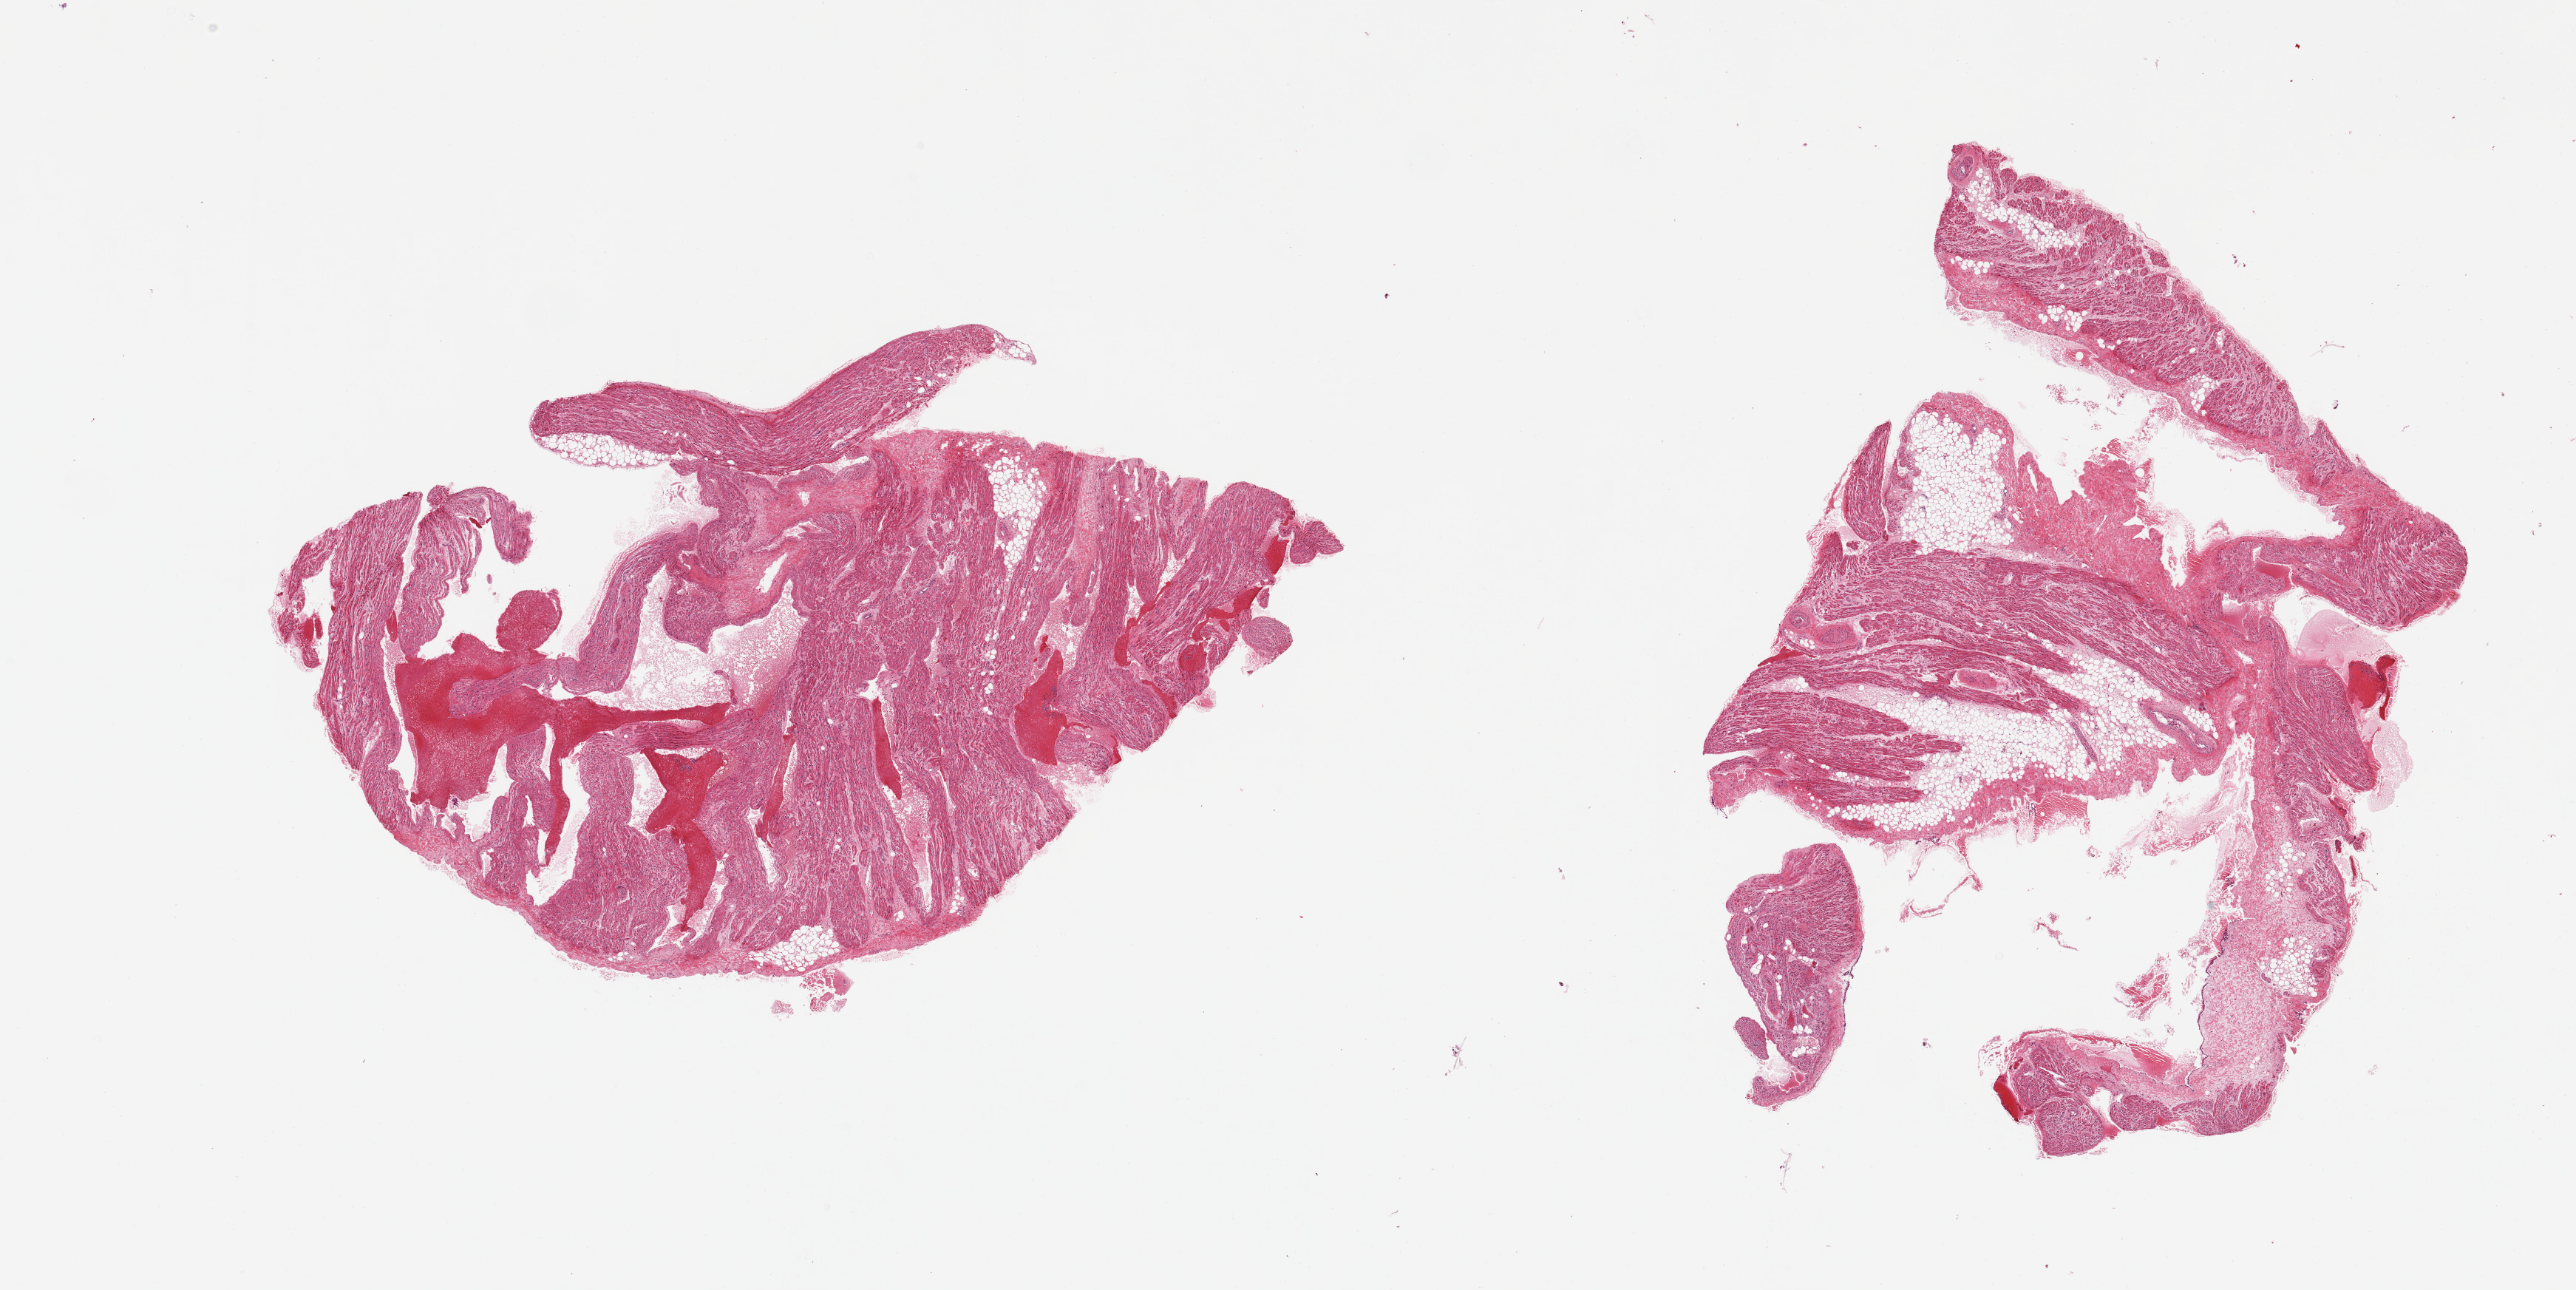
Digitized H&E-stained section, shown as a low-resolution overview of the whole scanned area (about 27.6 x 13.8 mm), PAXgene-fixed, paraffin-embedded tissue, section of auricular appendage (target tissue), donor tissue sample. Donor sex: female.
Review note (as recorded): 2 pieces; interstitial and patchy fibrosis.